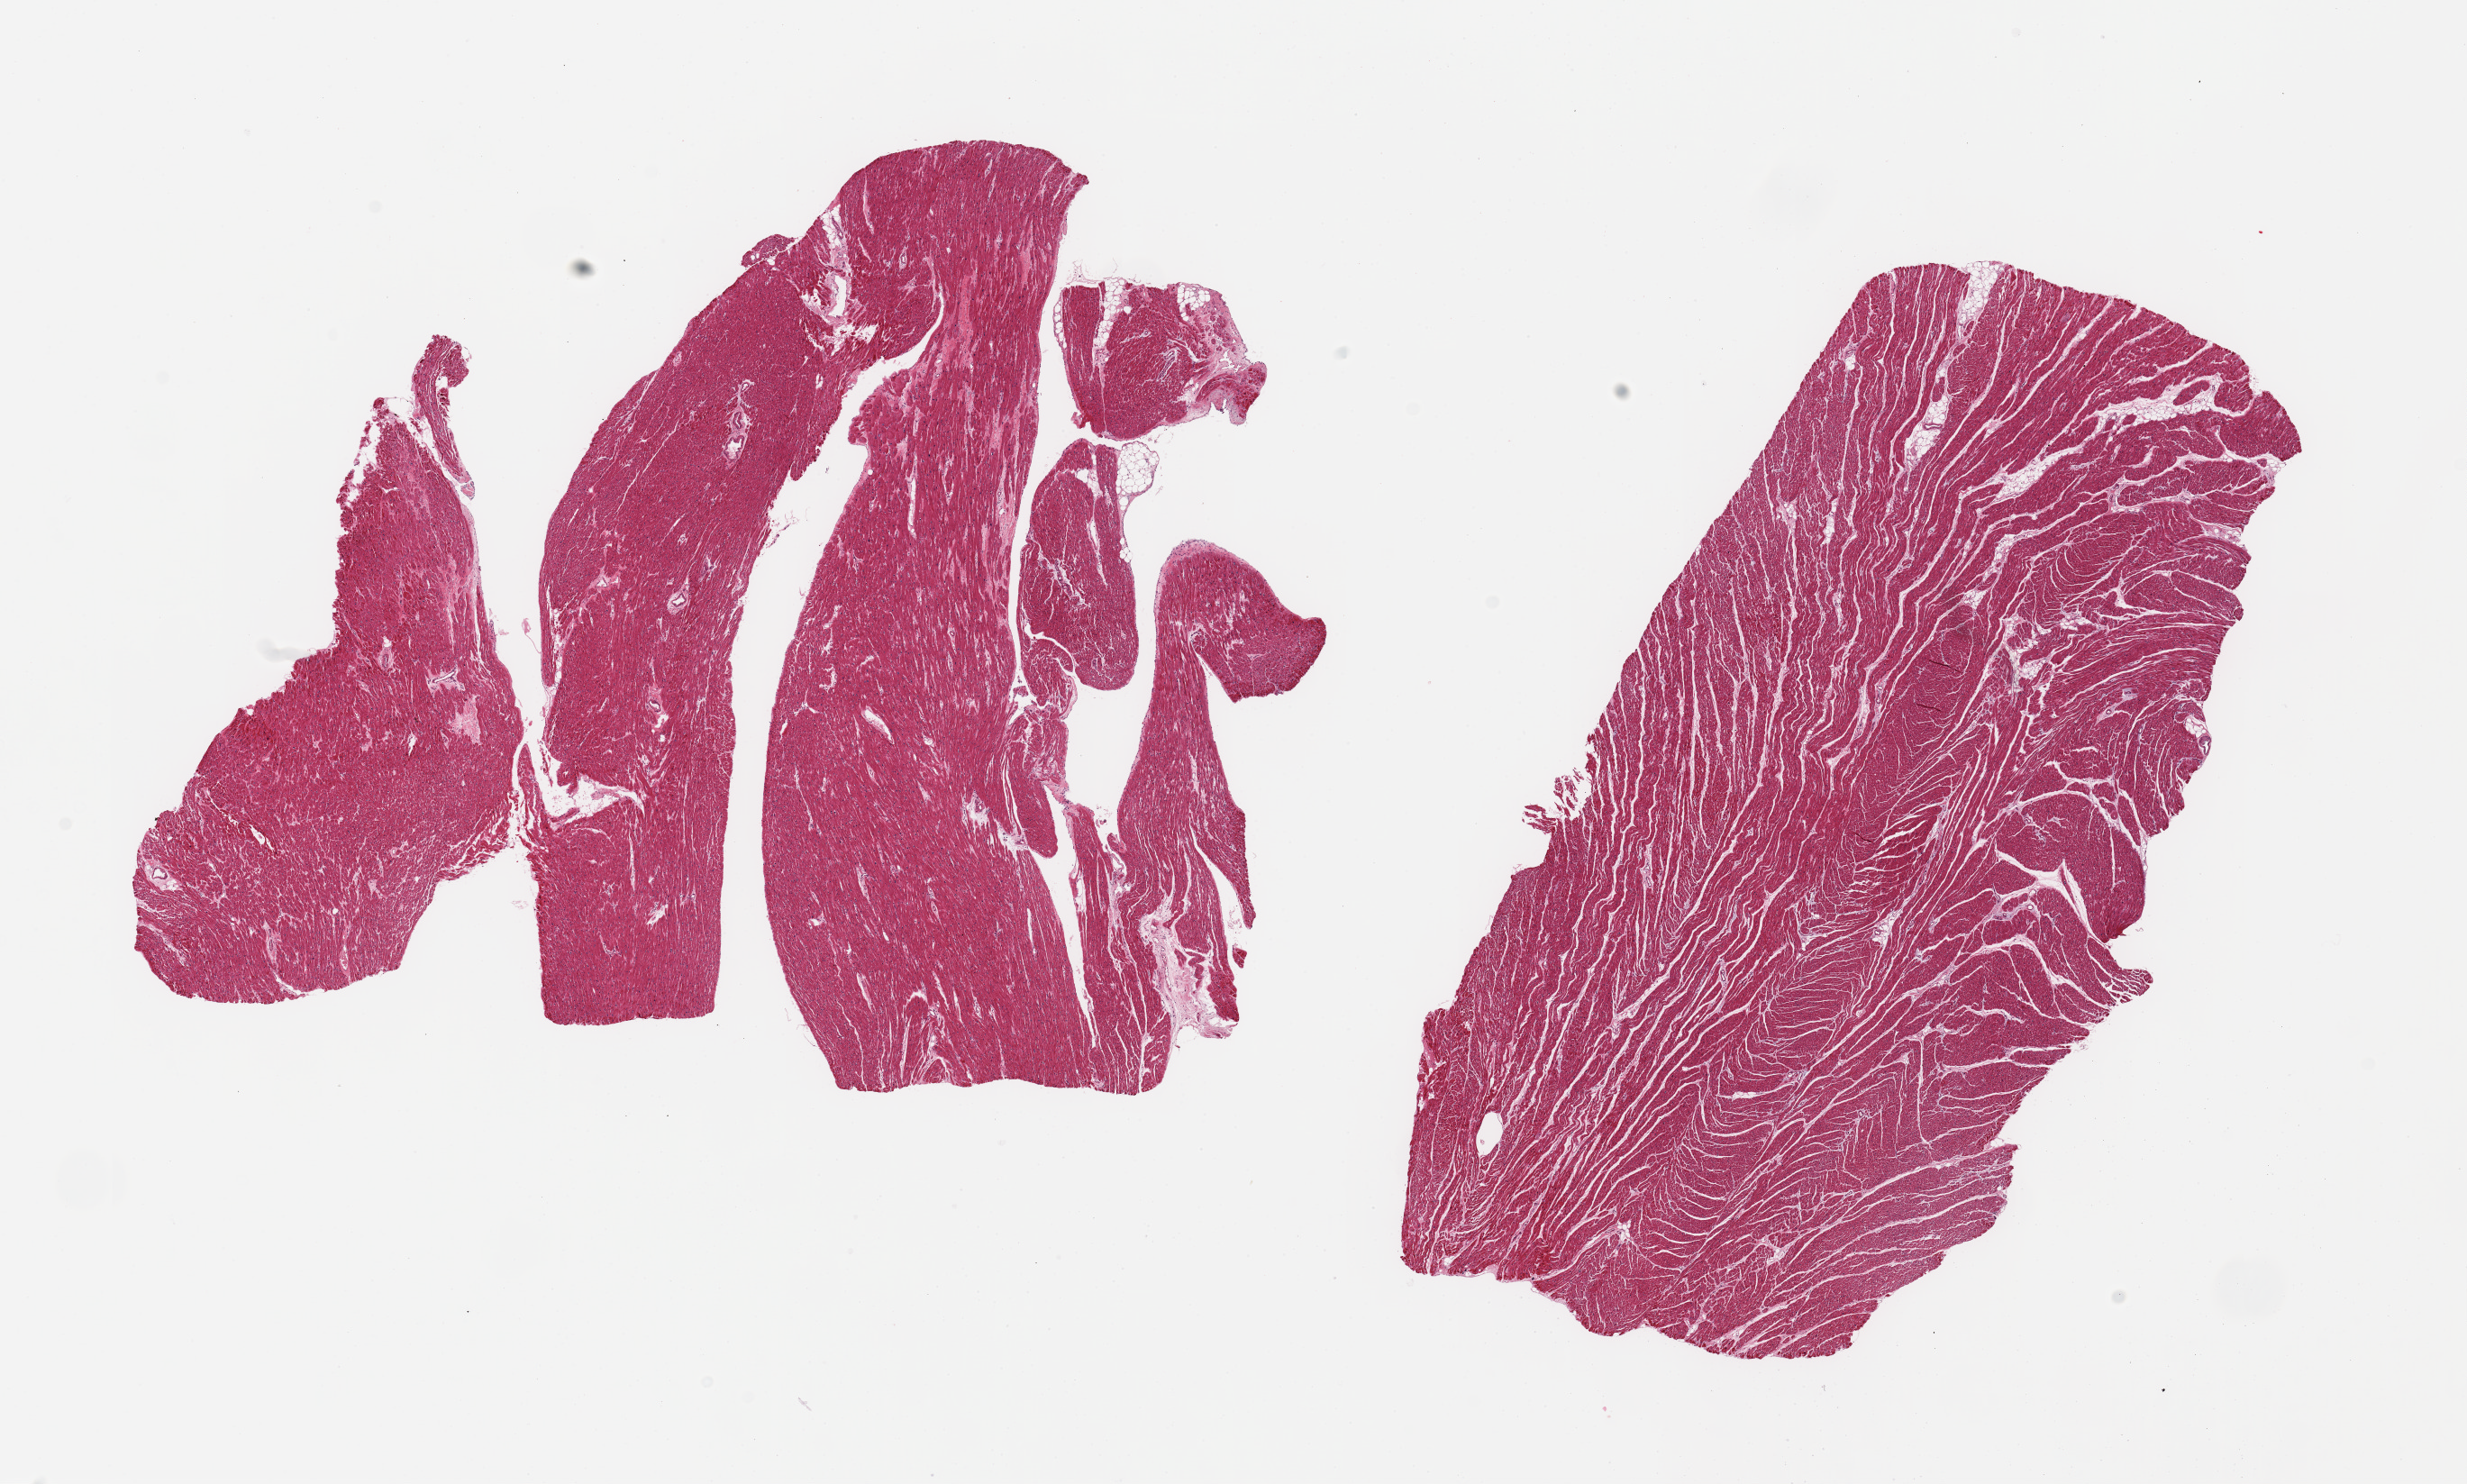
Haematoxylin and eosin whole-slide image, brightfield, low-resolution overview of the scanned area, about 21.7 x 13.0 mm (acquisition: 20x scan); PAXgene-fixed paraffin-embedded (PFPE) section; target tissue: heart; tissue donor sample. Donor sex: female.
Pathologist's review note for this sample: 2 pieces; nuclear enlargement, contraction bands.